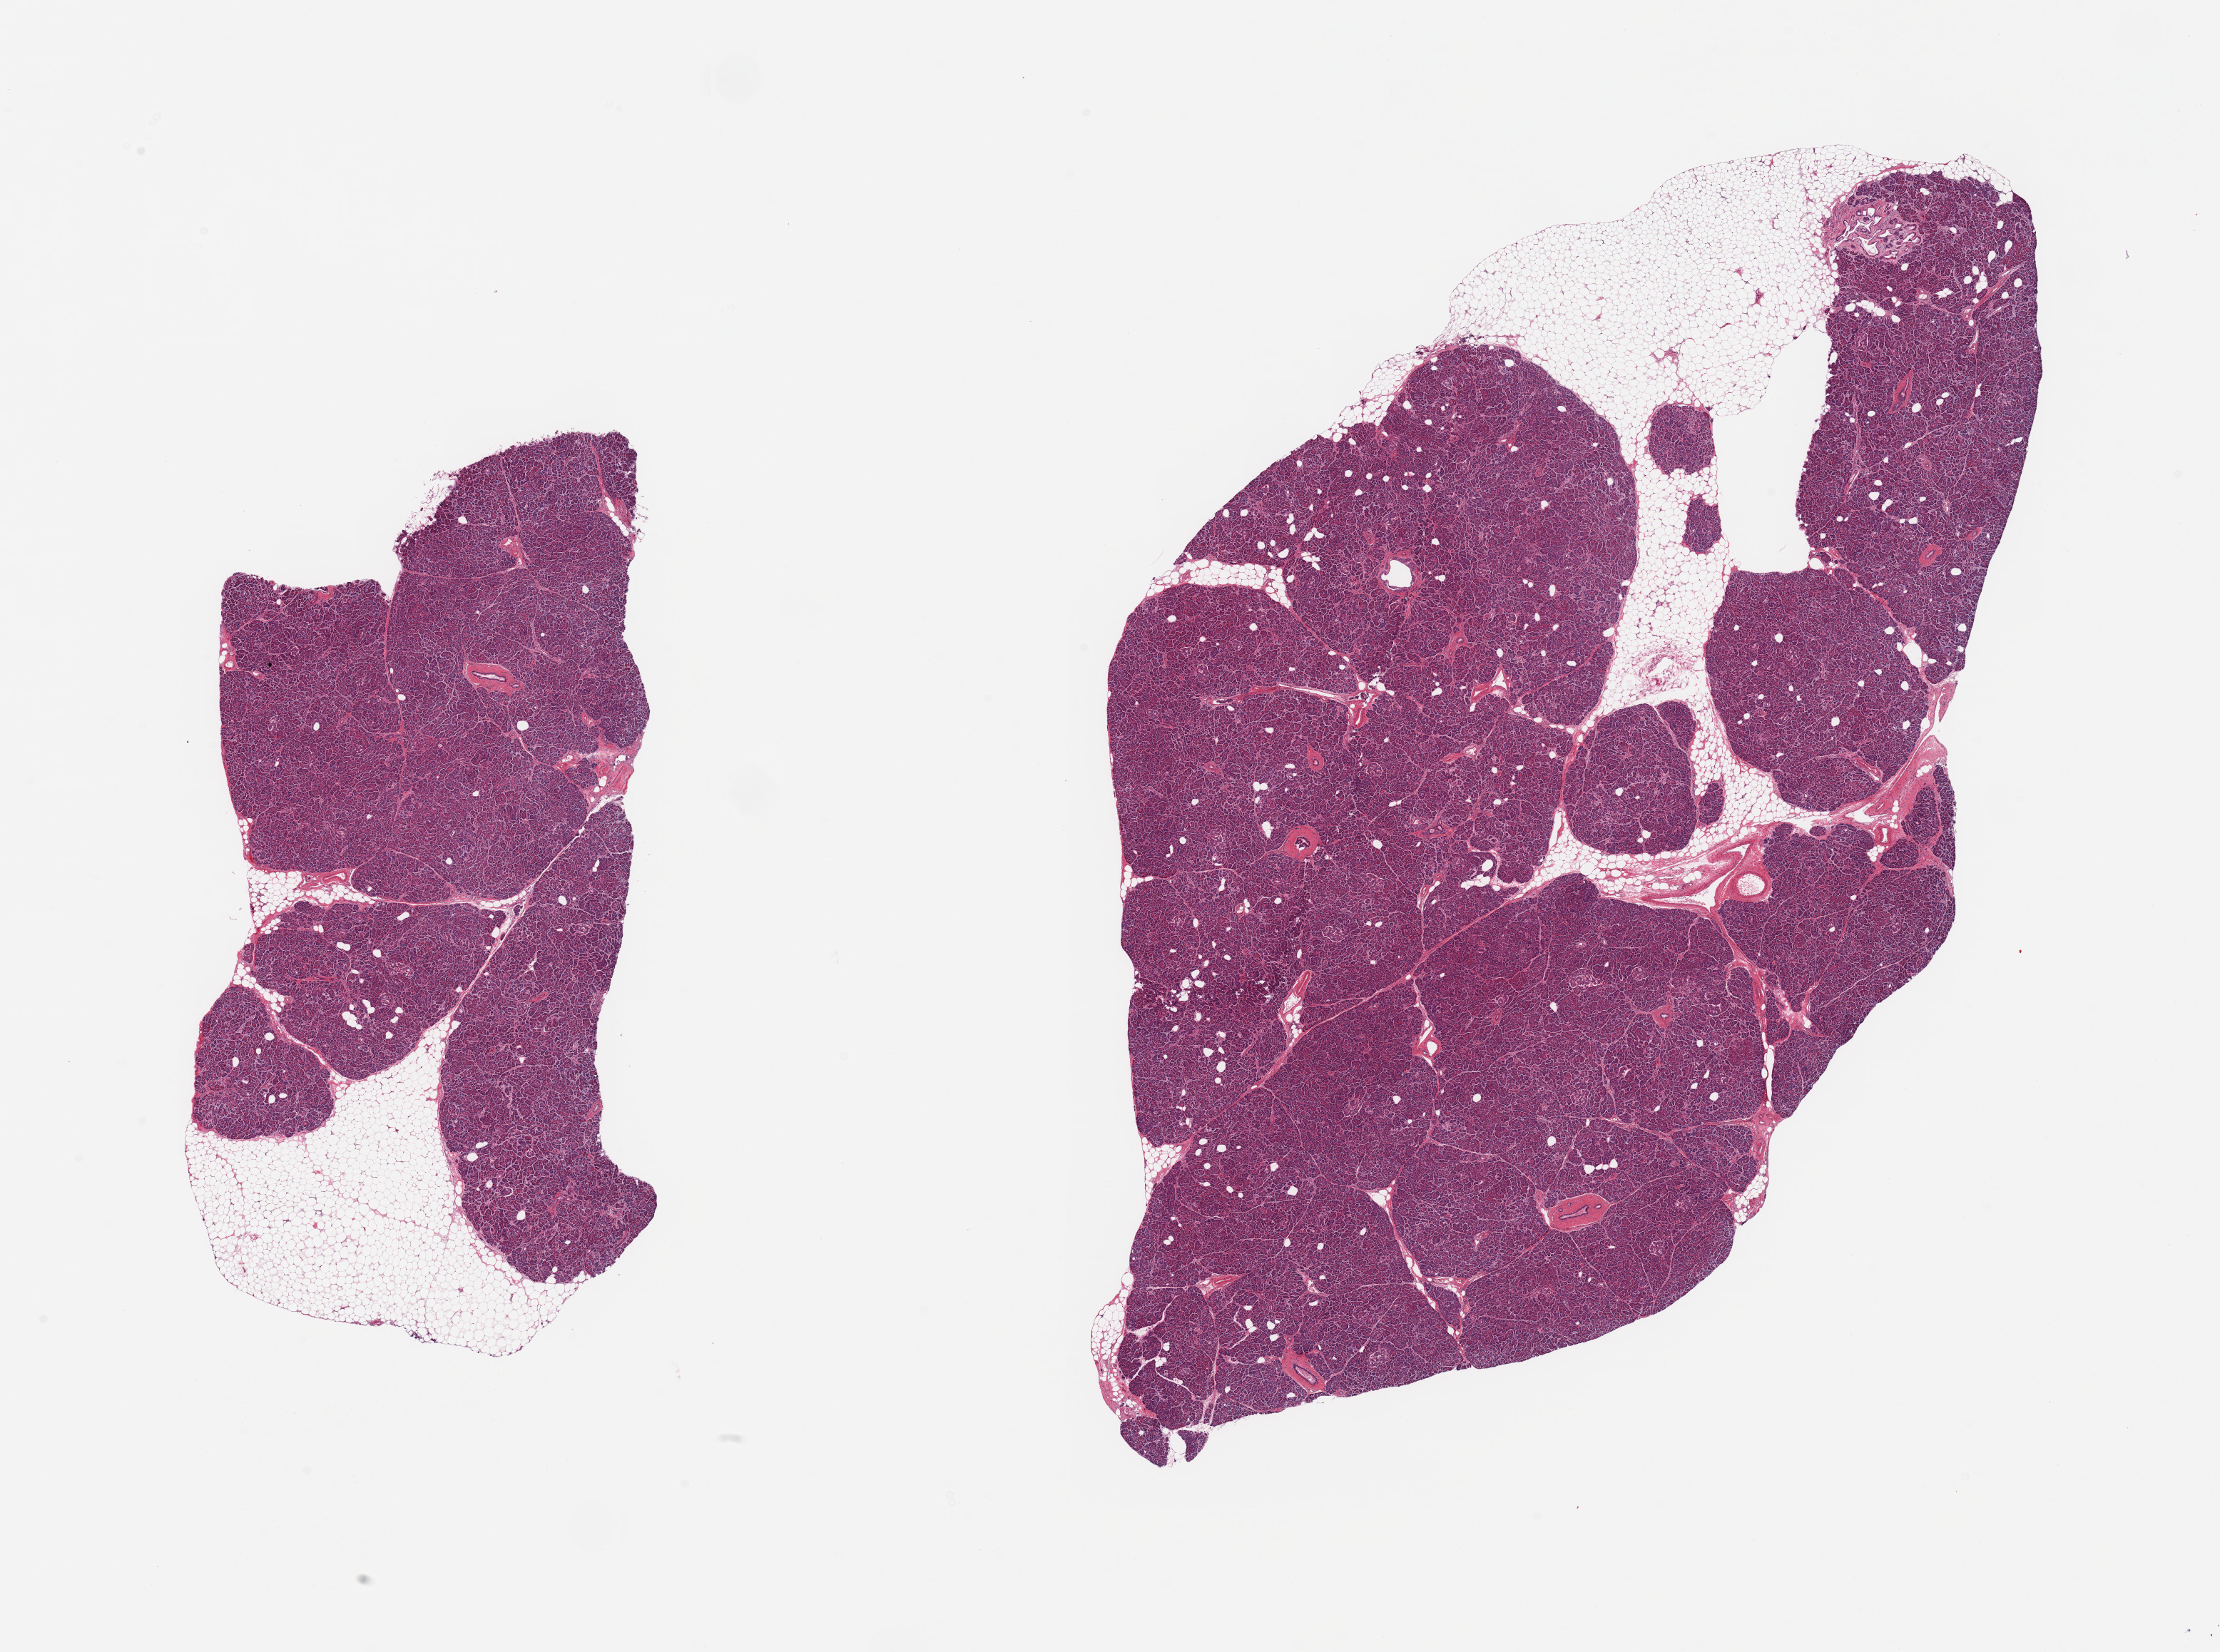
Whole-slide image, hematoxylin and eosin (H&E) stain — shown as a low-resolution overview of the whole scanned area (about 24.6 x 18.3 mm); PAXgene-fixed, paraffin-embedded tissue; section of pancreas (target tissue); donor tissue sample.
- pathologist's review note for this sample: 2 pieces; both include up to 20% attached fat, focal squamous metaplasia of duct